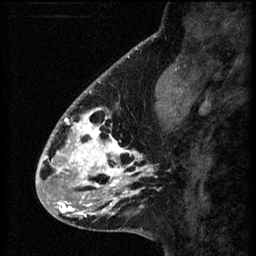
Breast MRI (dynamic contrast-enhanced), one sagittal slice; slice 19 of 60 in the series (ordered by position); 3 images stored at this slice position (order not interpretable as contrast timing); 1.5 T; TE 4.2 ms, TR 8.2 ms; 256 × 256 image matrix, field of view 180 × 180 mm. Female patient, age 41 years.
Outlined on this slice (semi-automatic segmentation, software-assisted and operator-edited):
- analysis volume of interest (the breast-tissue region the enhancement analysis was run in; not a lesion): box from (x=56, y=104) to (x=157, y=207) px
- tumour enhancement mask (voxels above the 70 % enhancement threshold inside the analysis volume of interest): (x=56, y=106)–(x=154, y=205)